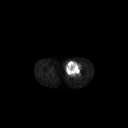
FDG PET of an extremity soft-tissue mass (from a PET/CT study), one axial slice; position 238 of 267 along the scan axis; 3.27 mm slice thickness; 128 × 128 image matrix, field of view 700 × 700 mm. Male patient, age 63 years. Case-level facts recorded for this patient, not image findings: histological type: pleiomorphic liposarcoma; grade: high; site of the primary tumour: left thigh.
Annotated regions visible in this slice (expert contour drawn on MRI and transferred to this co-registered scan by the dataset authors):
- gross tumour volume including surrounding oedema: bounding box (x1, y1, x2, y2) in pixels: (65, 61, 82, 76)
- gross tumour volume (mass): (66, 61, 80, 76)